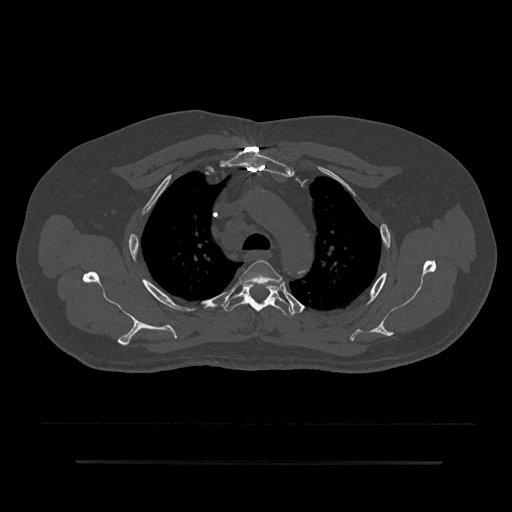
CT including the spine, one axial slice. Position 633 of 797 along the scan axis. 120 kVp. Bone window (W 1800 / L 400 HU). 512 × 512 image matrix, field of view 464 × 464 mm. Male patient, age 59 years. Case-level facts recorded for this patient, not image findings: primary cancer: bile ducts; vertebrae with lytic lesions (as recorded): T10.
Outlined on this slice (semi-automatically segmented with operator editing):
- T3 vertebra: bounding box (x1, y1, x2, y2) in pixels: (239, 260, 283, 287)
- T4 vertebra: (222, 283, 294, 317)